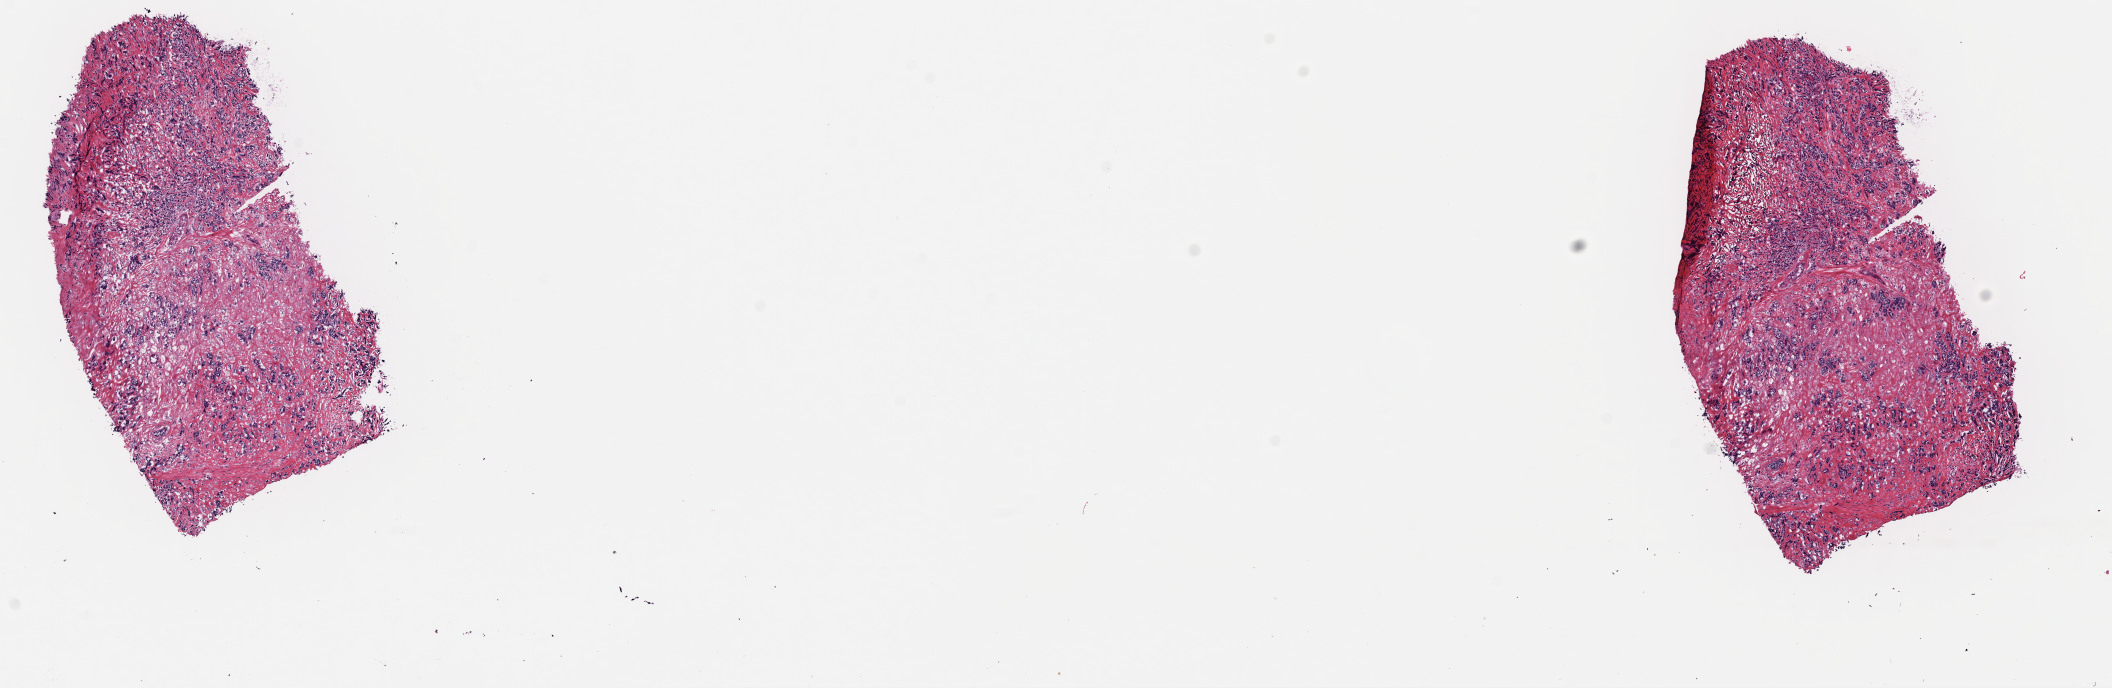
Digitized H&E tissue section (whole slide) — low-resolution overview of the scanned area, about 16.7 x 5.4 mm (acquisition: 40x scan); frozen section from the top of the tissue portion; sample: primary tumour, breast. Patient: female, age at initial diagnosis 62 years. Slide review estimates, as recorded: tumour cells 45%, tumour nuclei 75%, normal cells 0%, stromal cells 55%, necrosis 0%. Infiltration values recorded for this section: lymphocyte infiltration 1%, monocyte infiltration 0%, neutrophil infiltration 0%.
AJCC pathologic stage: III (6th edition). Lymph nodes positive (case pathology): 5 of 18 examined. Laterality: right. Pathologic diagnosis: Lobular carcinoma, NOS.